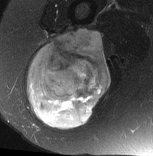
MRI of an extremity soft-tissue mass, one axial slice; slice 39 of 77 in the series (ordered by position); T2-weighted fat-saturated; MR volume resampled by the dataset authors to the PET/CT grid (not the native acquisition matrix); 153 × 156 image matrix, field of view 149 × 152 mm. Female patient. From the clinical record (not read from this slice): histological type: synovial sarcoma; grade: intermediate; site of the primary tumour: right buttock.
Annotated regions visible in this slice (expert contour drawn on MRI and transferred to this co-registered scan by the dataset authors):
- gross tumour volume including surrounding oedema: bounding box (x1, y1, x2, y2) in pixels: (28, 29, 111, 130)
- gross tumour volume (mass): (28, 29, 111, 130)